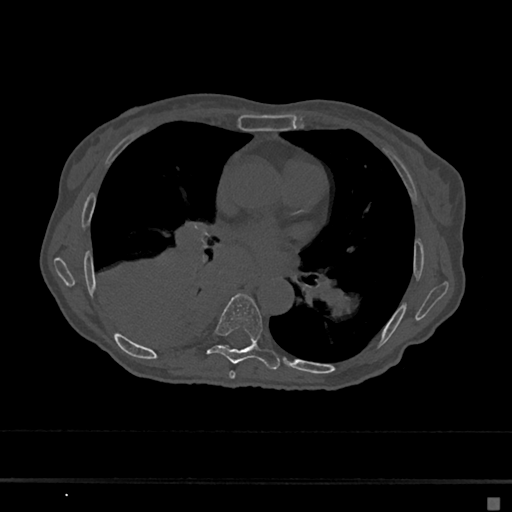
CT including the spine, one axial slice. Slice 372 of 797 in the series (ordered by position). Reconstruction kernel Br40s/3. Bone window (W 1800 / L 400 HU). 0.5 mm slice thickness. 512 × 512 image matrix. Female patient, age 68 years. Case-level facts recorded for this patient, not image findings: primary cancer: renal.
Annotated regions visible in this slice (semi-automatically segmented with operator editing):
- T6 vertebra: bounding box <229,371,236,379> (left, top, right, bottom; pixels)
- T7 vertebra: <206,294,280,370>